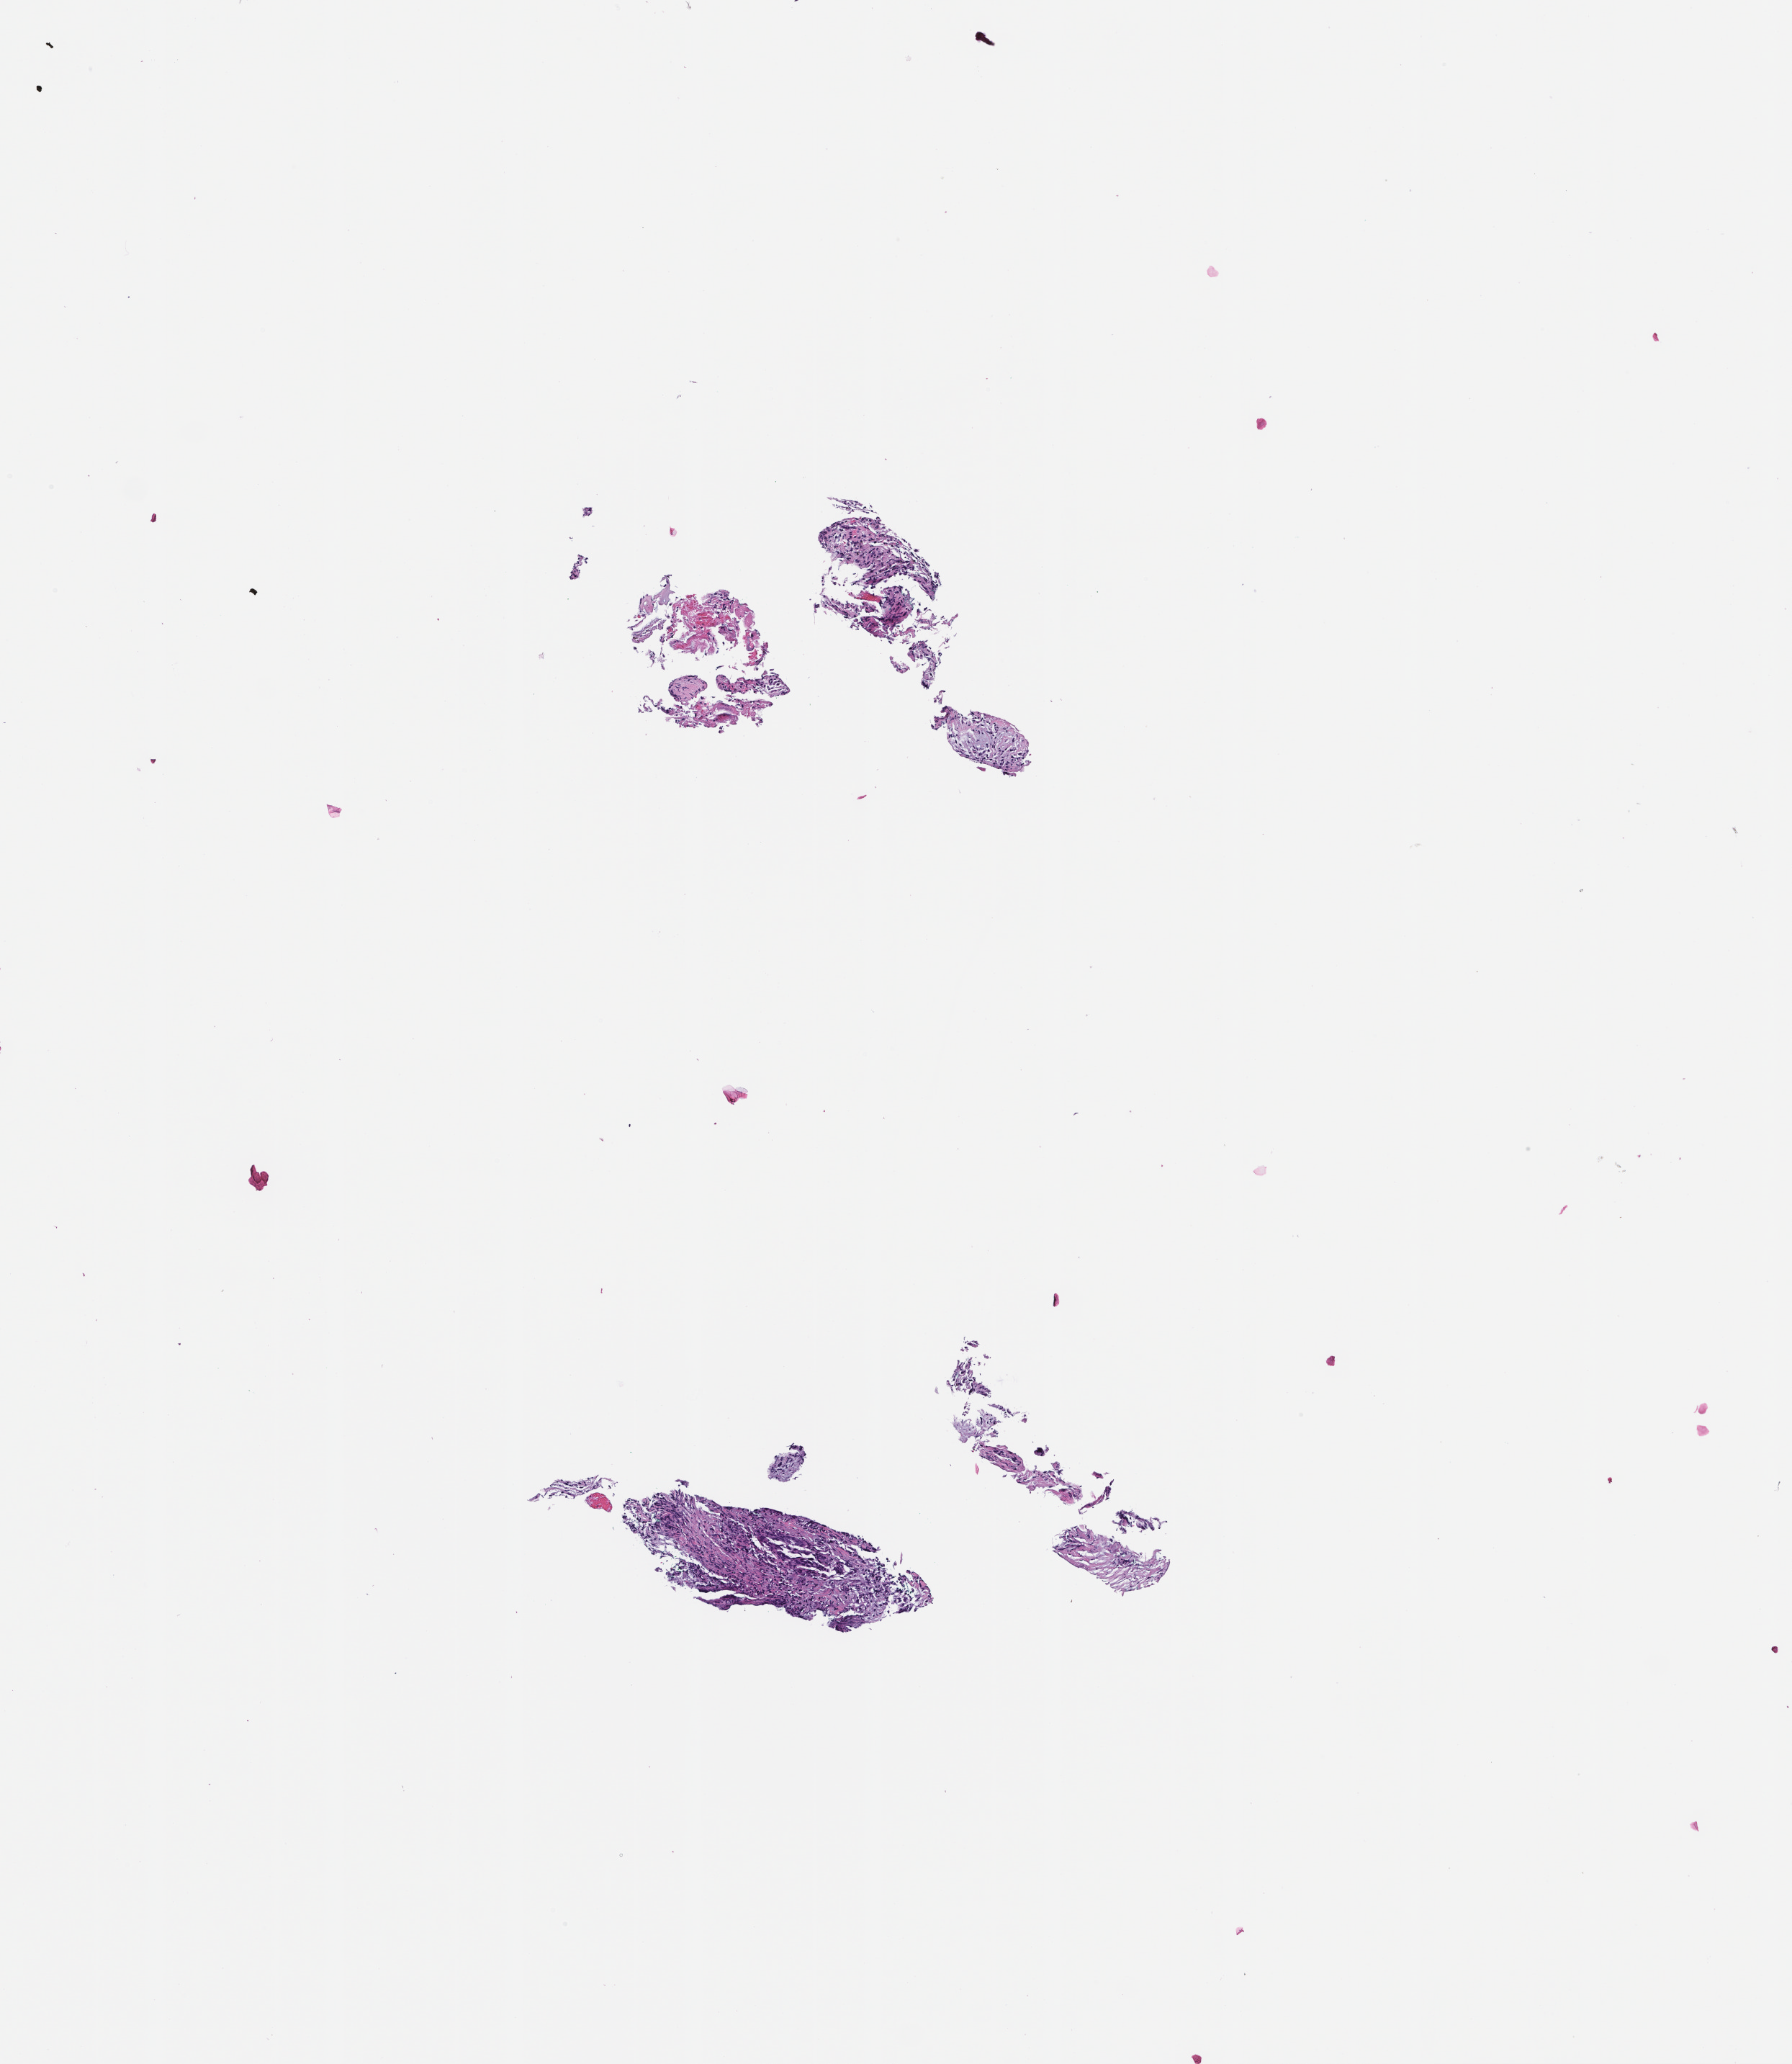
Haematoxylin and eosin whole-slide image, shown as a low-resolution overview of the whole scanned area (about 5.0 x 5.8 mm); formalin-fixed paraffin-embedded section; specimen time point: archival tissue. Female patient.
- this section: metastatic tumor tissue
- patient diagnosis (primary): Non-Small Cell Lung Carcinoma